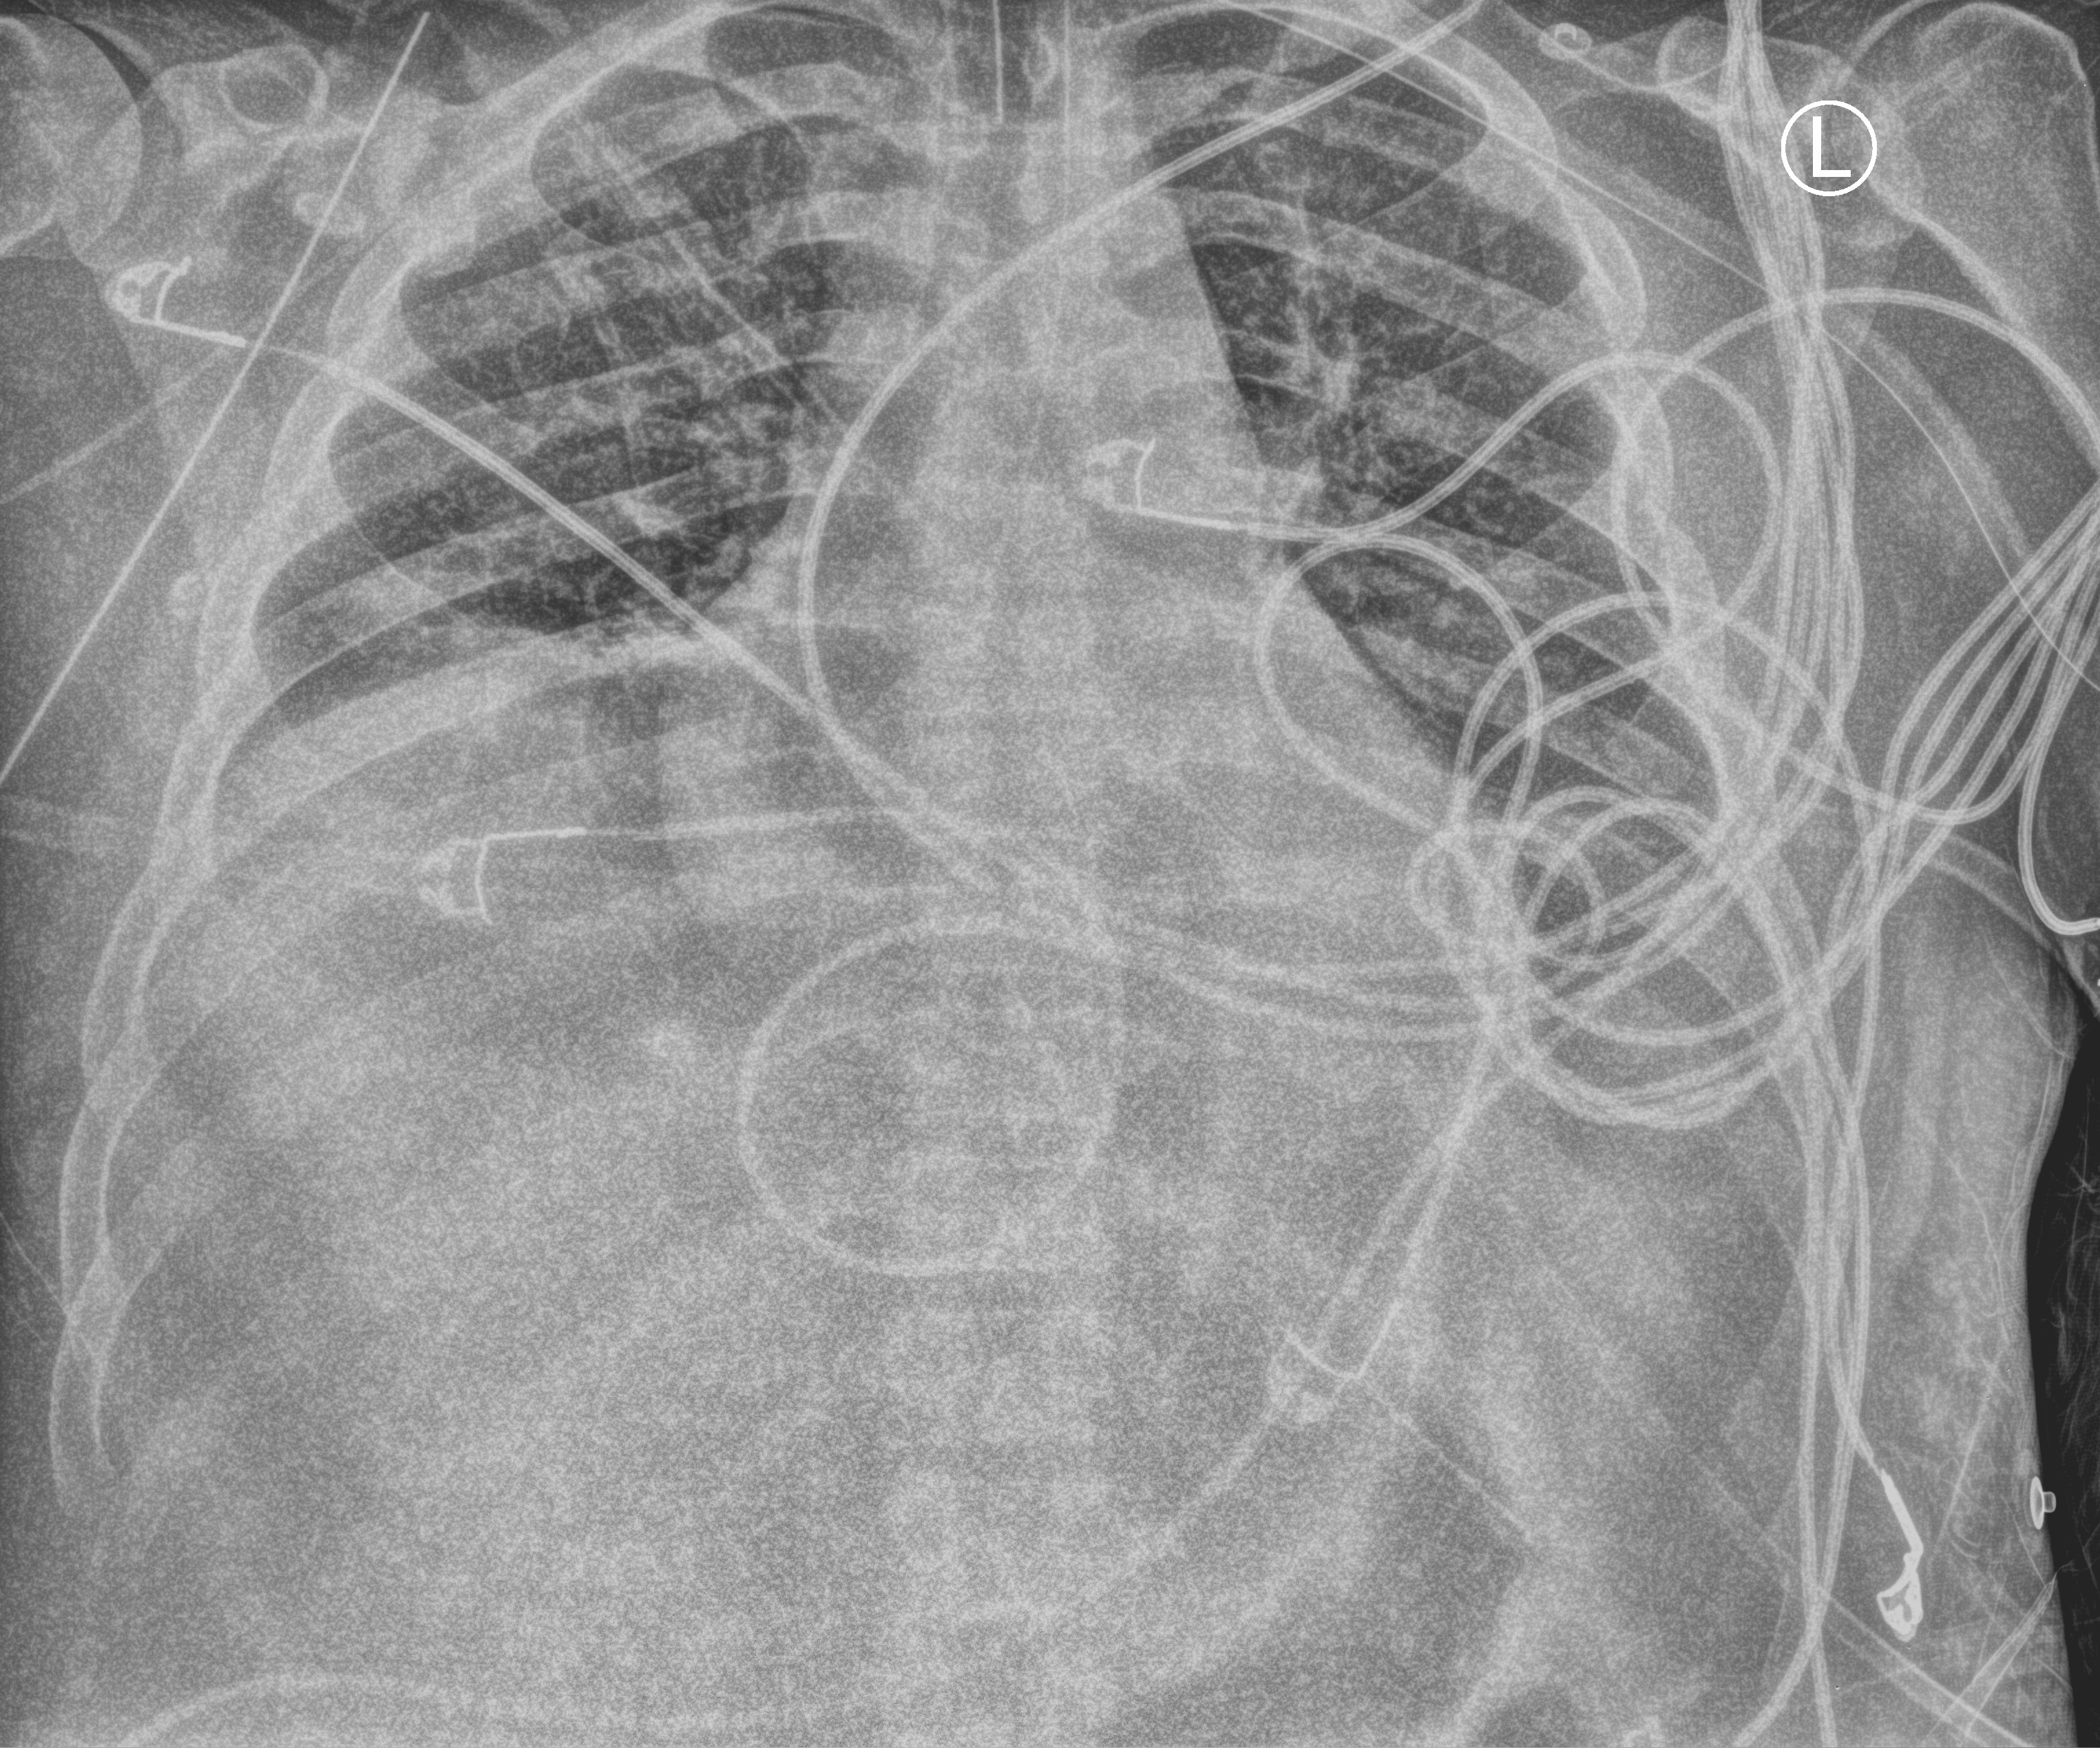
Bedside chest radiograph (computed radiography), anteroposterior (AP) projection. Patient hospitalised with COVID-19; male, aged 18–59 years.
Hospital-stay facts (about this admission, not read from this image; timing relative to this image not recorded):
- mechanically ventilated during this hospital stay: yes
- chronic kidney disease (admission record): no
- hypertension (admission record): yes